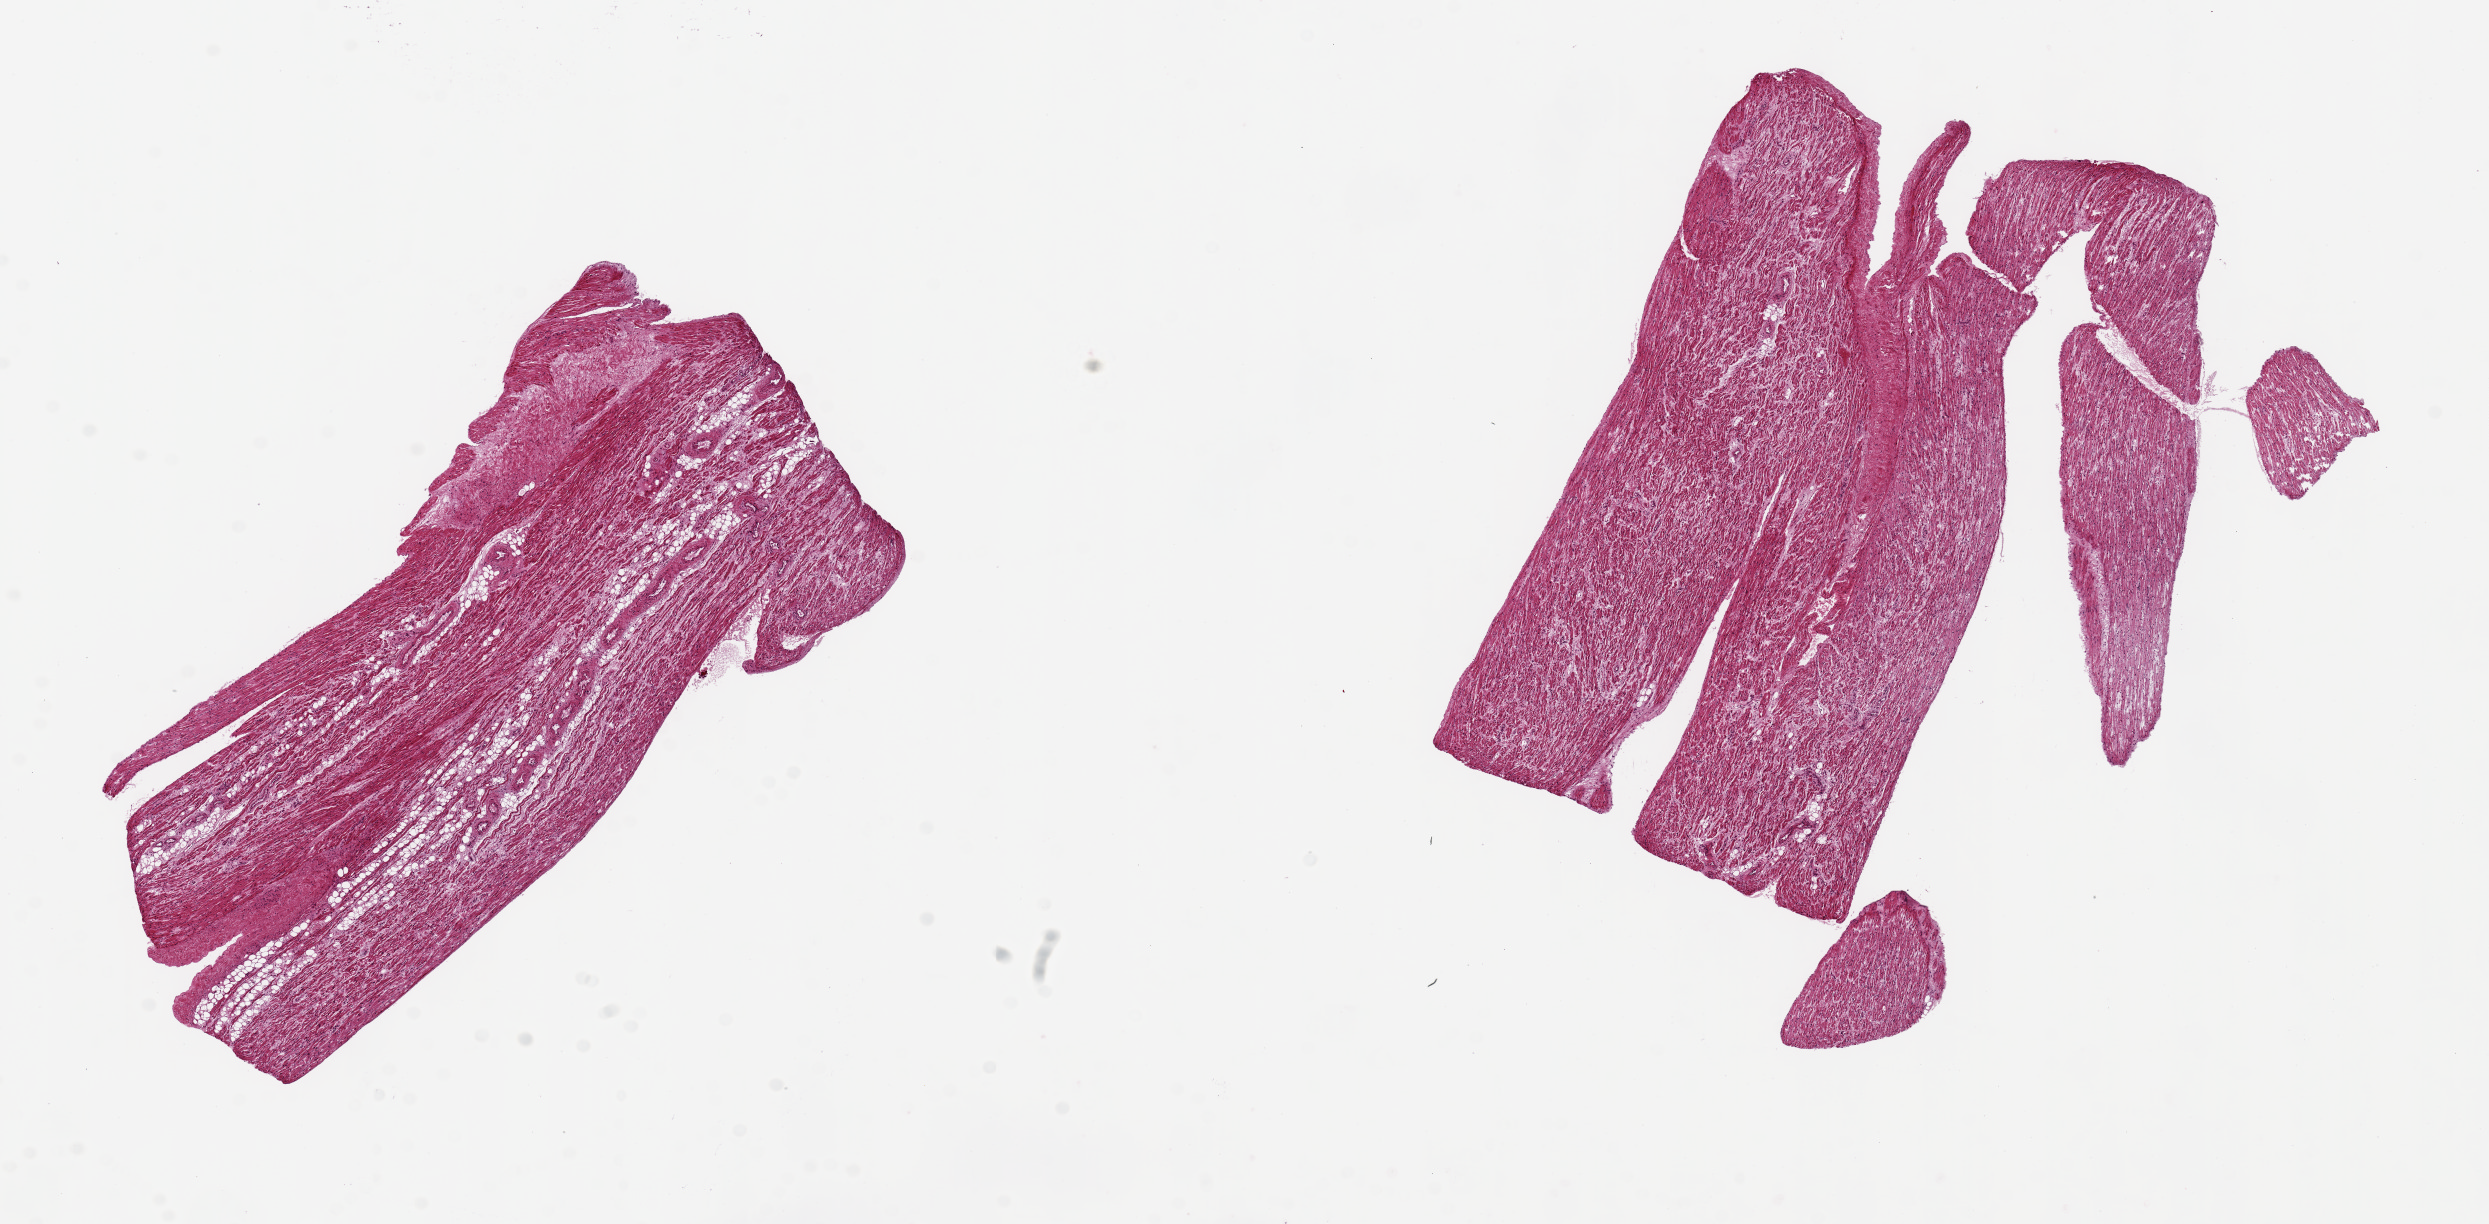
Digitized haematoxylin and eosin-stained section — whole scanned area (about 19.7 x 9.7 mm) shown as a low-resolution overview, PAXgene-fixed, paraffin-embedded tissue, section of auricular appendage (target tissue), tissue donor sample. Female donor.
* pathologist's review note for this sample: 2 pieces ~6x4mm